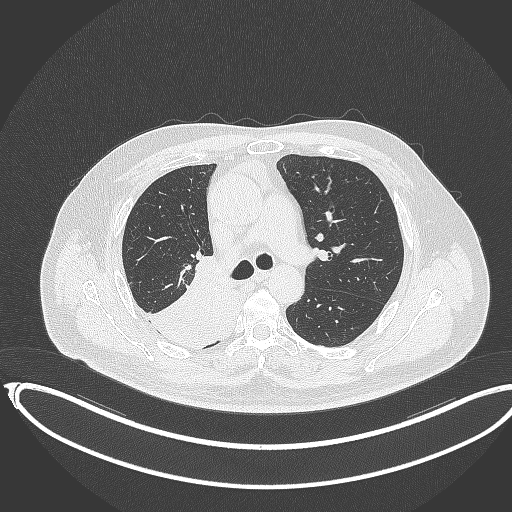
Chest CT, one axial slice; slice 233 of 403 in the series (ordered by position); reconstruction kernel B70f; 120 kVp; lung window (W 1500 / L -600 HU); 512 × 512 image matrix. Male patient, age 68 years. From the clinical record (not read from this slice): clinical TNM (as recorded): T2a N0 M0.
Annotated regions visible in this slice (rectangle marked by the reading radiologist):
- lung tumour (recorded histology: adenocarcinoma): bounding box [x1, y1, x2, y2] px = [144, 259, 234, 354]